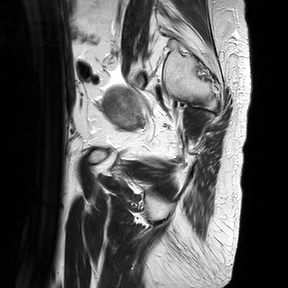
Pelvic MRI for cervical cancer, one sagittal slice. Slice 5 of 30 in the series (ordered by position). T2-weighted. 1.5 T. TE 100 ms, TR 4816.3 ms. 4 mm slice thickness. 288 × 288 image matrix, field of view 300 × 300 mm. Patient: female, 74 years.
Annotated regions visible in this slice (outlined manually by an expert reader):
- uterus and cervix: bounding box <102,86,146,130> (left, top, right, bottom; pixels)